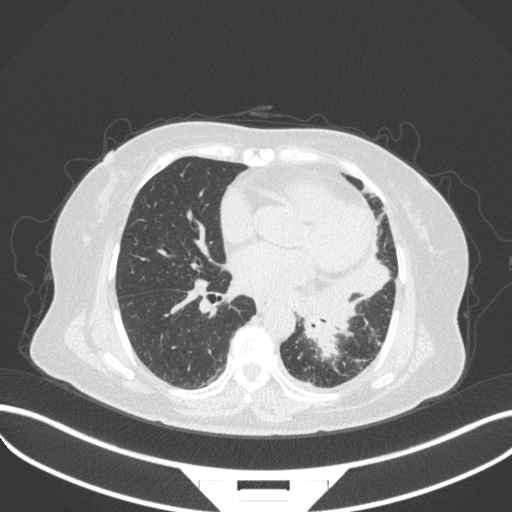
Chest CT, one axial slice; slice 157 of 328 in the series (ordered by position); reconstruction kernel B31f; 120 kVp; lung window (W 1500 / L -600 HU); 512 × 512 image matrix. Female patient, age 69 years. Case-level facts recorded for this patient, not image findings: clinical TNM (as recorded): T2b N3 M1.
Outlined on this slice (bounding box drawn by a radiologist):
- lung tumour (recorded histology: adenocarcinoma): bounding box [x1, y1, x2, y2] px = [284, 273, 359, 361]